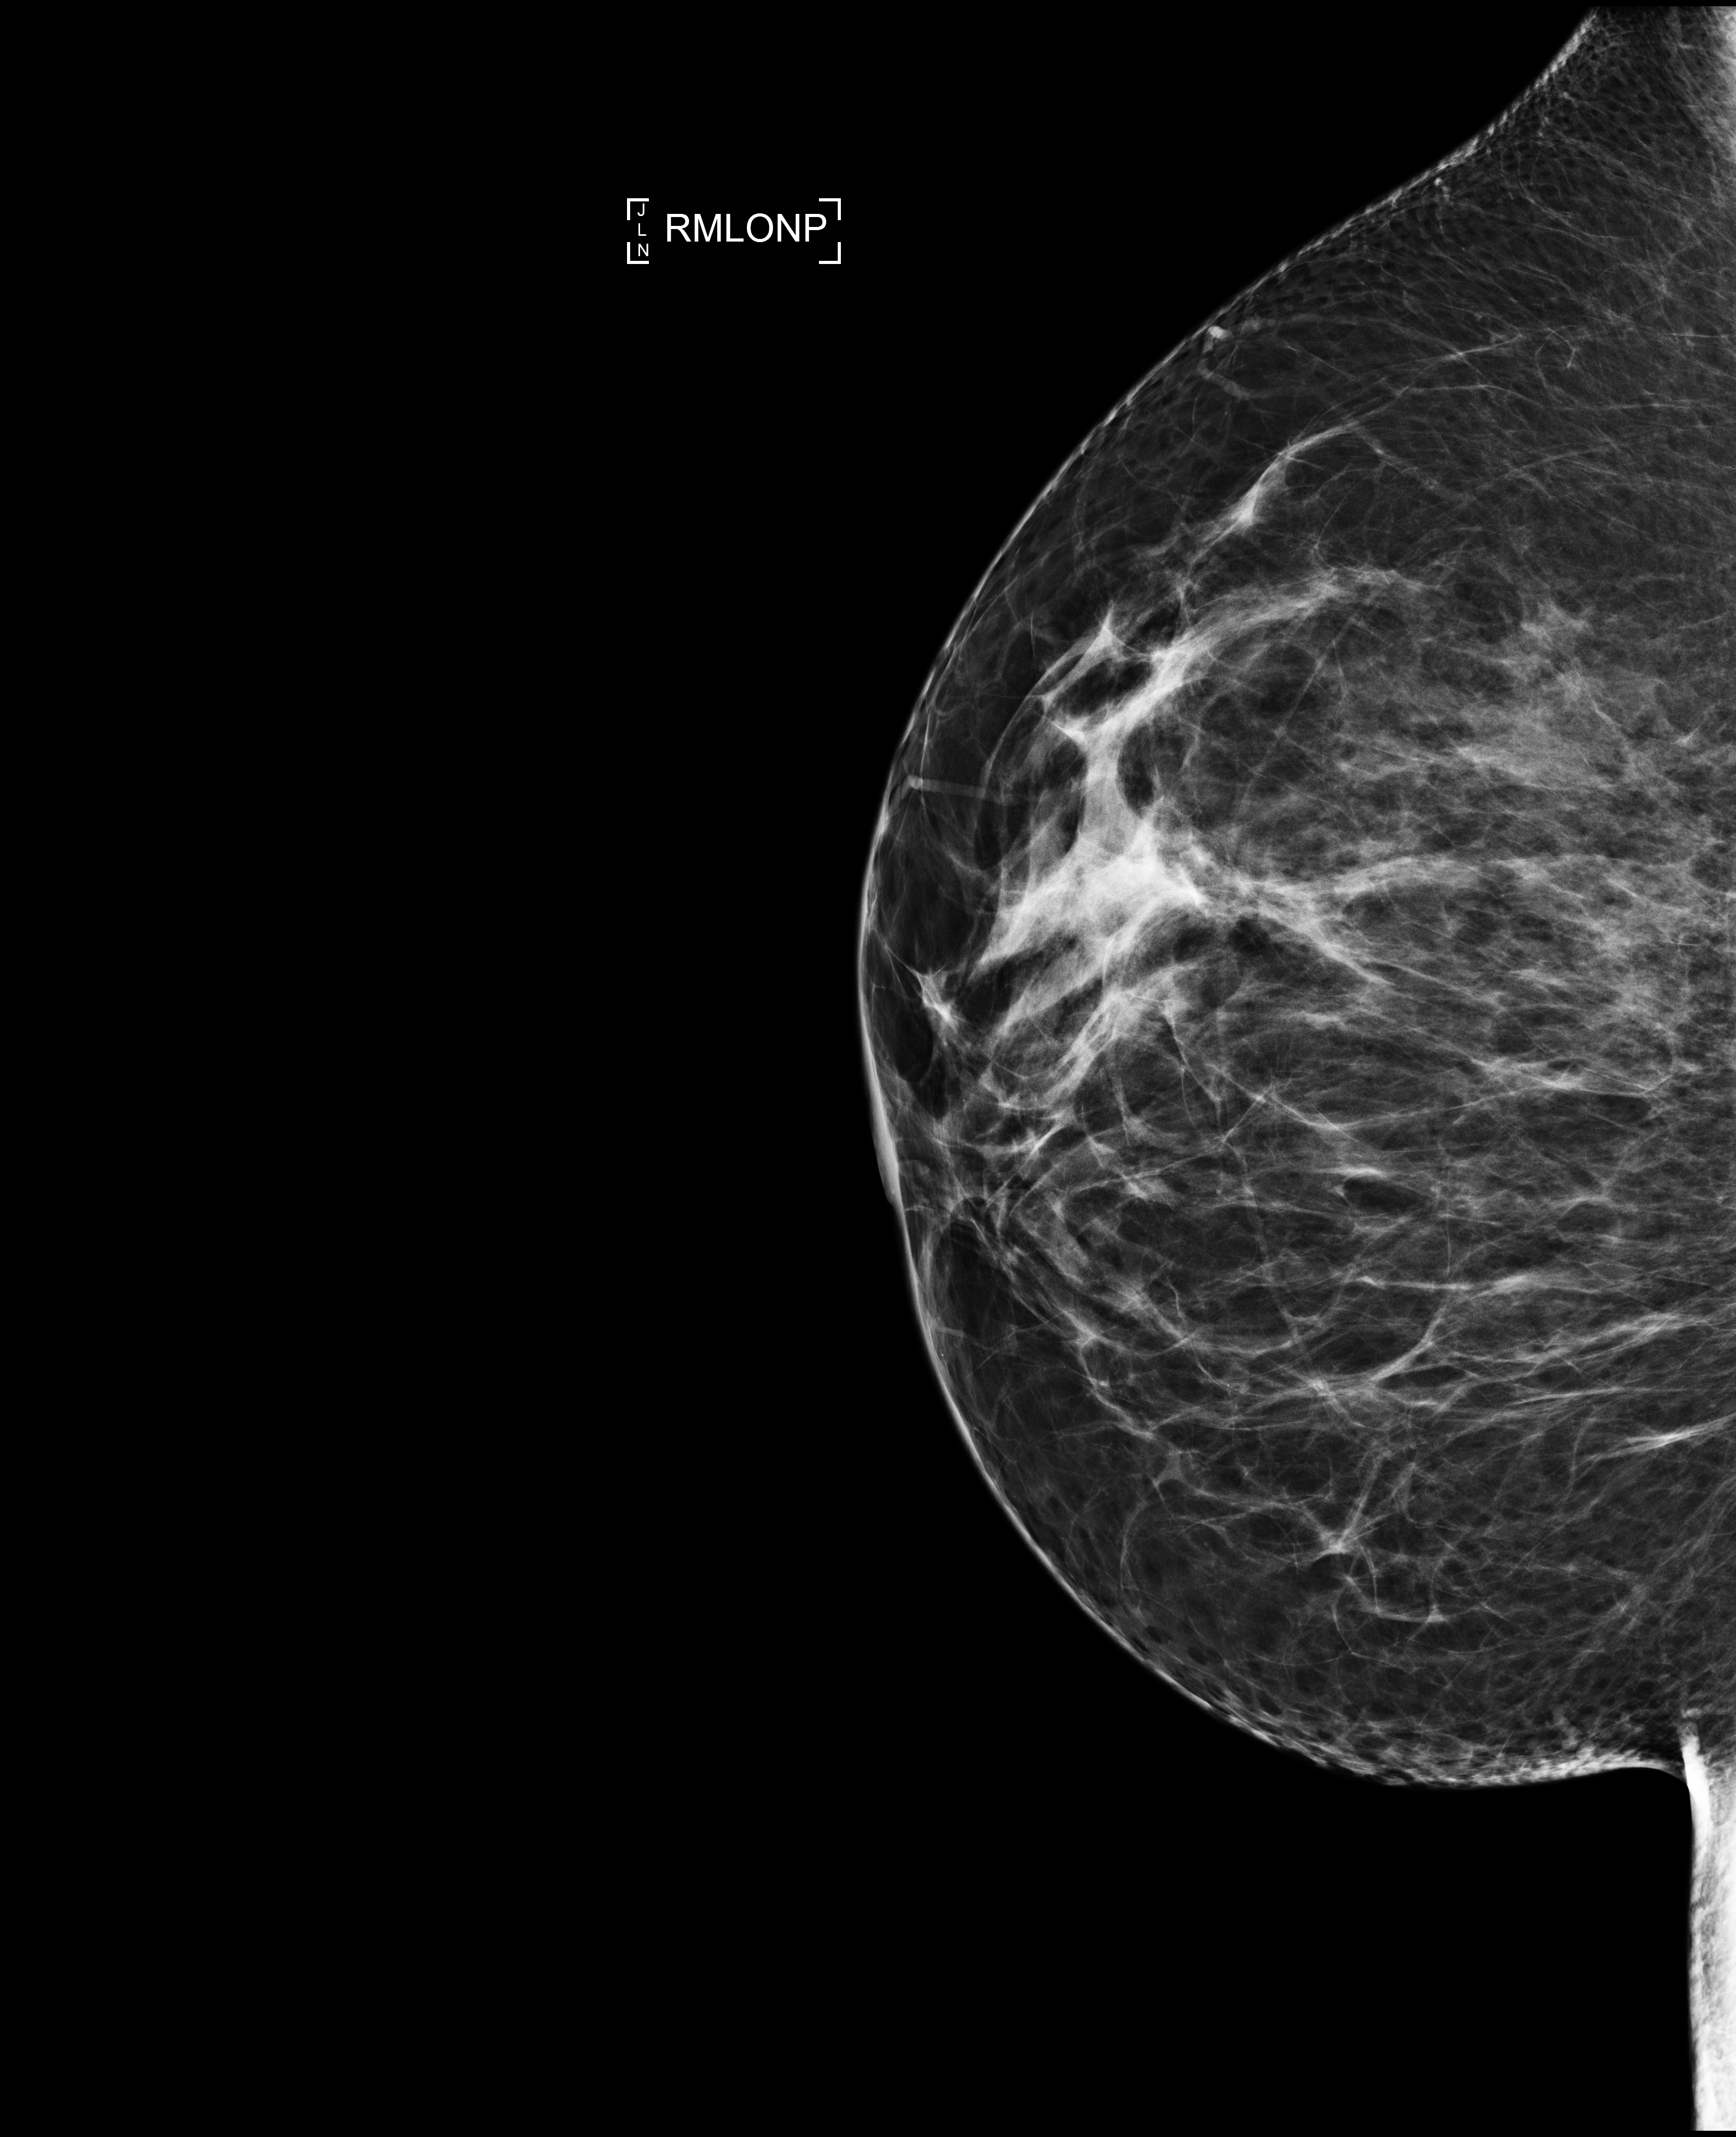
Annual screening mammography examination; system: Selenia Dimensions. Patient: female, 52 years.
Image type: full-field digital mammogram. Breast: right. Projection: mediolateral oblique (MLO) view, nipple in profile.